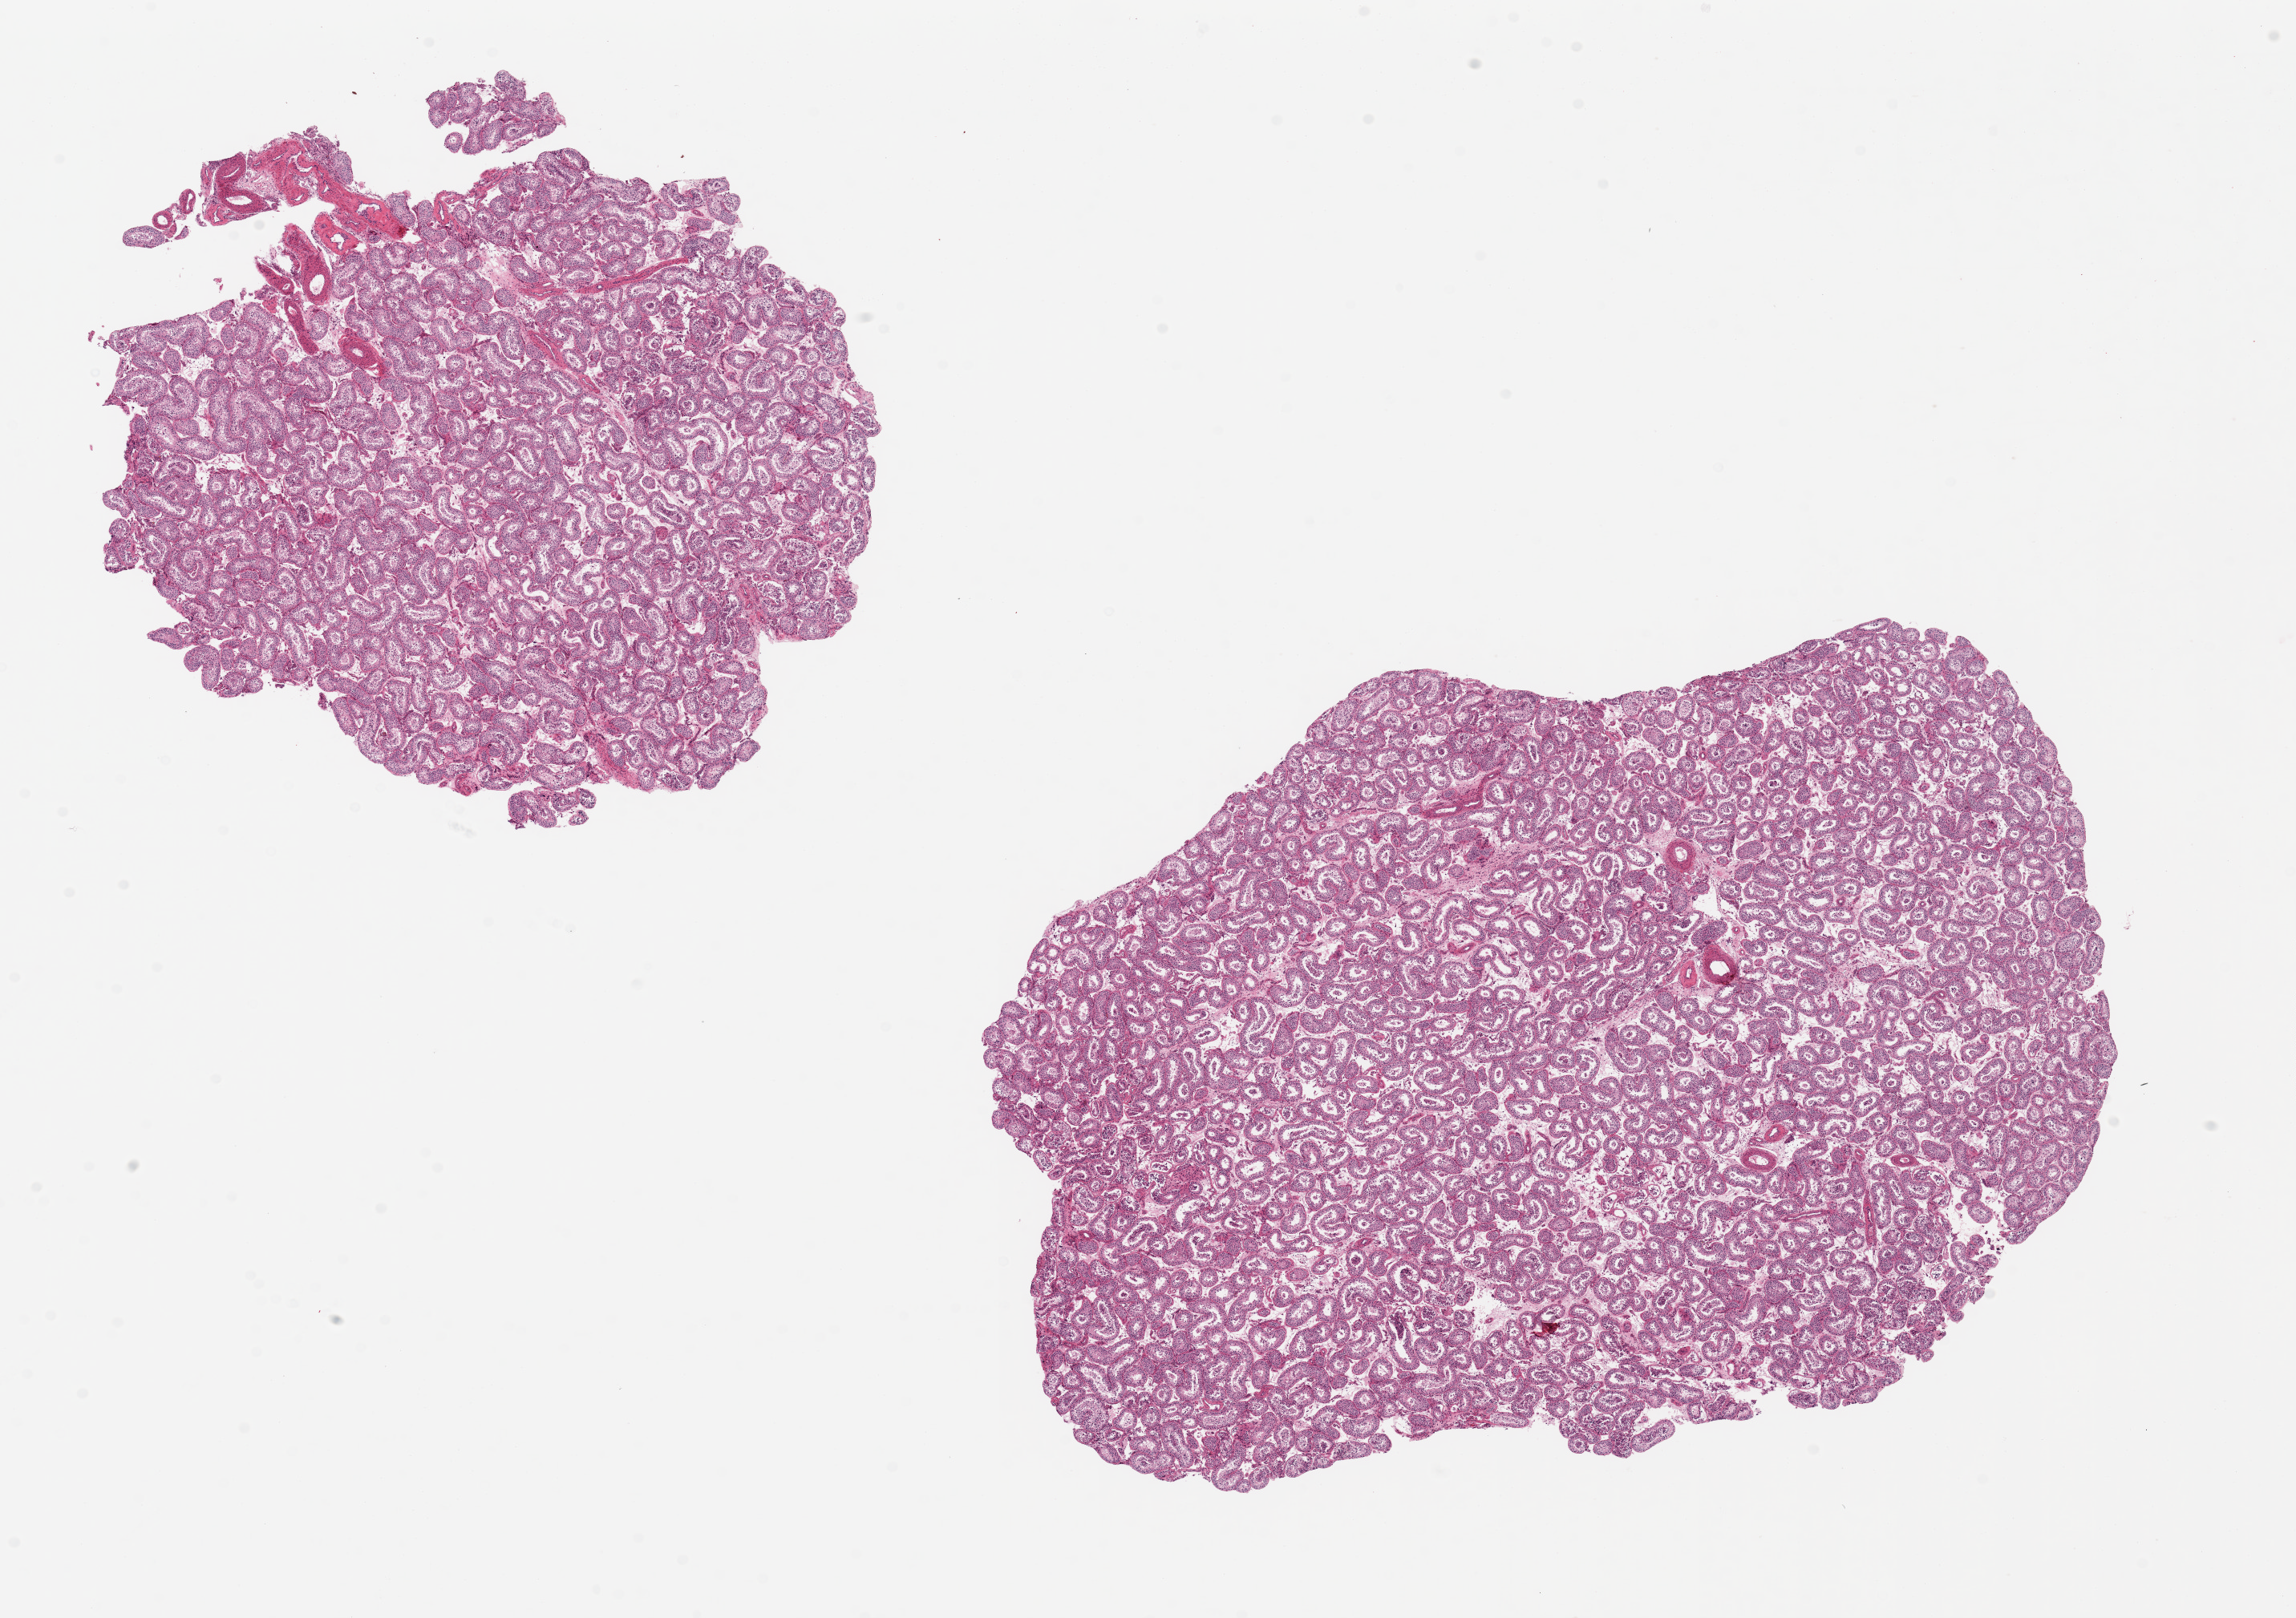
Whole-slide image, hematoxylin and eosin (H&E) stain — a low-resolution overview of the entire scanned area, about 22.6 x 16.0 mm (acquisition: 20x scan); PAXgene-fixed, paraffin-embedded tissue; sampled site (target tissue): testis; donor tissue sample. Donor: male.
- review note (as recorded): 2 pieces, ~9x7mm. Spermatogenesis present